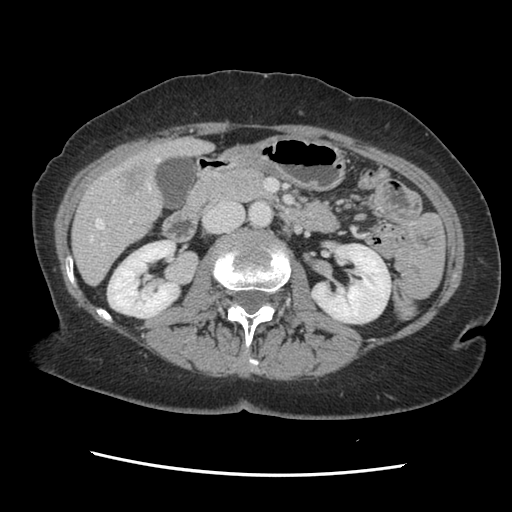
Contrast-enhanced abdominal CT, one axial slice. Slice 59 of 141 in the series (ordered by position). 120 kVp. Soft-tissue window (W 400 / L 40 HU). 2.5 mm slice thickness. 512 × 512 image matrix, field of view 330 × 330 mm. Female patient, age 61 years. Case-level facts recorded for this patient, not image findings: diagnosis: colorectal cancer liver metastases, imaged before liver resection; multiple liver metastases: no; largest metastasis: 2.4 cm; disease in both lobes: no.
Outlined on this slice (expert manual segmentation):
- hepatic veins: box from (x=90, y=158) to (x=159, y=241) px
- liver: (x=73, y=139)–(x=209, y=283)
- planned liver remnant (the part of the liver to remain after resection): (x=73, y=192)–(x=161, y=283)
- portal vein (with intrahepatic branches): (x=102, y=182)–(x=138, y=245)
- liver metastasis: (x=117, y=167)–(x=145, y=191)